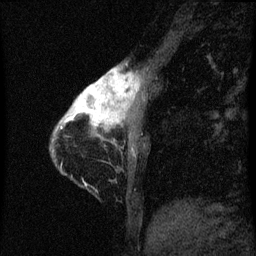
Breast MRI (dynamic contrast-enhanced), one sagittal slice. Position 11 of 60 along the scan axis. Dynamic contrast-enhanced series, image 2 of 3 at this slice position (ordered by acquisition). 1.5 T. TE 4.2 ms, TR 8 ms. 2 mm slice thickness. 256 × 256 image matrix, field of view 180 × 180 mm. Patient: female, 38 years.
Outlined on this slice (semi-automatic segmentation, software-assisted and operator-edited):
- analysis volume of interest (the breast-tissue region the enhancement analysis was run in; not a lesion): bounding box [x1, y1, x2, y2] px = [61, 68, 141, 147]
- tumour enhancement mask (voxels above the 70 % enhancement threshold inside the analysis volume of interest): [61, 68, 139, 129]